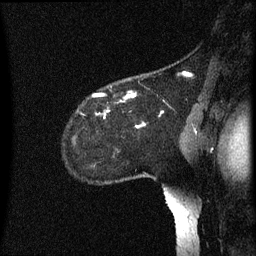
Breast MRI (dynamic contrast-enhanced), one sagittal slice. Position 49 of 60 along the scan axis. Dynamic contrast-enhanced series, image 2 of 3 at this slice position (ordered by acquisition). 1.5 T. TE 4.2 ms, TR 8.4 ms. 2.2 mm slice thickness. 256 × 256 image matrix. Patient: female, 35 years. Case-level facts recorded for this patient, not image findings: setting: breast cancer imaged before/during neoadjuvant chemotherapy; receptor status: HER2-positive.
Outlined on this slice (semi-automatically segmented with operator editing):
- analysis volume of interest (the breast-tissue region the enhancement analysis was run in; not a lesion): bounding box (x1, y1, x2, y2) in pixels: (68, 74, 165, 169)
- tumour enhancement mask (voxels above the 70 % enhancement threshold inside the analysis volume of interest): (94, 92, 140, 129)